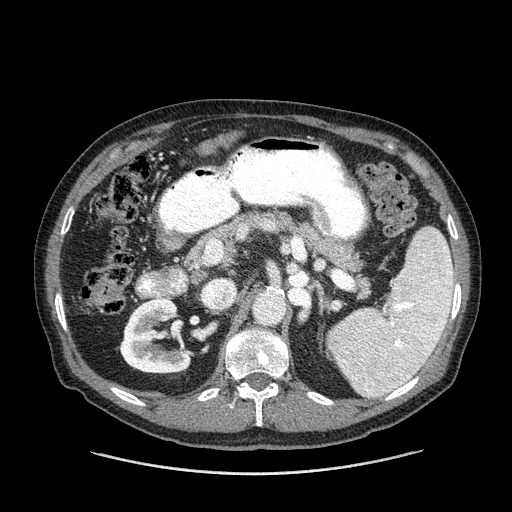
Contrast-enhanced abdominal CT (liver protocol), one axial slice. Slice 58 of 180 in the series (ordered by position). Reconstruction kernel STANDARD. One of 2 acquisitions stored at this slice position. Soft-tissue window (W 400 / L 40 HU). 512 × 512 image matrix, field of view 420 × 420 mm. From the clinical record (not read from this slice): diagnosis: hepatocellular carcinoma (patient treated with transarterial chemoembolisation; whether this scan precedes or follows treatment is not stated here); TNM stage (as recorded): Stage-II; Child-Pugh class: A; tumour differentiation: well differentiated; tumour nodularity: multinodular.
Structures marked on this image (semi-automatic segmentation, software-assisted and operator-edited):
- liver parenchyma outside the tumour (the mass and vessels are separate outlines, so this box may not span the whole liver): bounding box (x1, y1, x2, y2) in pixels: (202, 142, 212, 152)